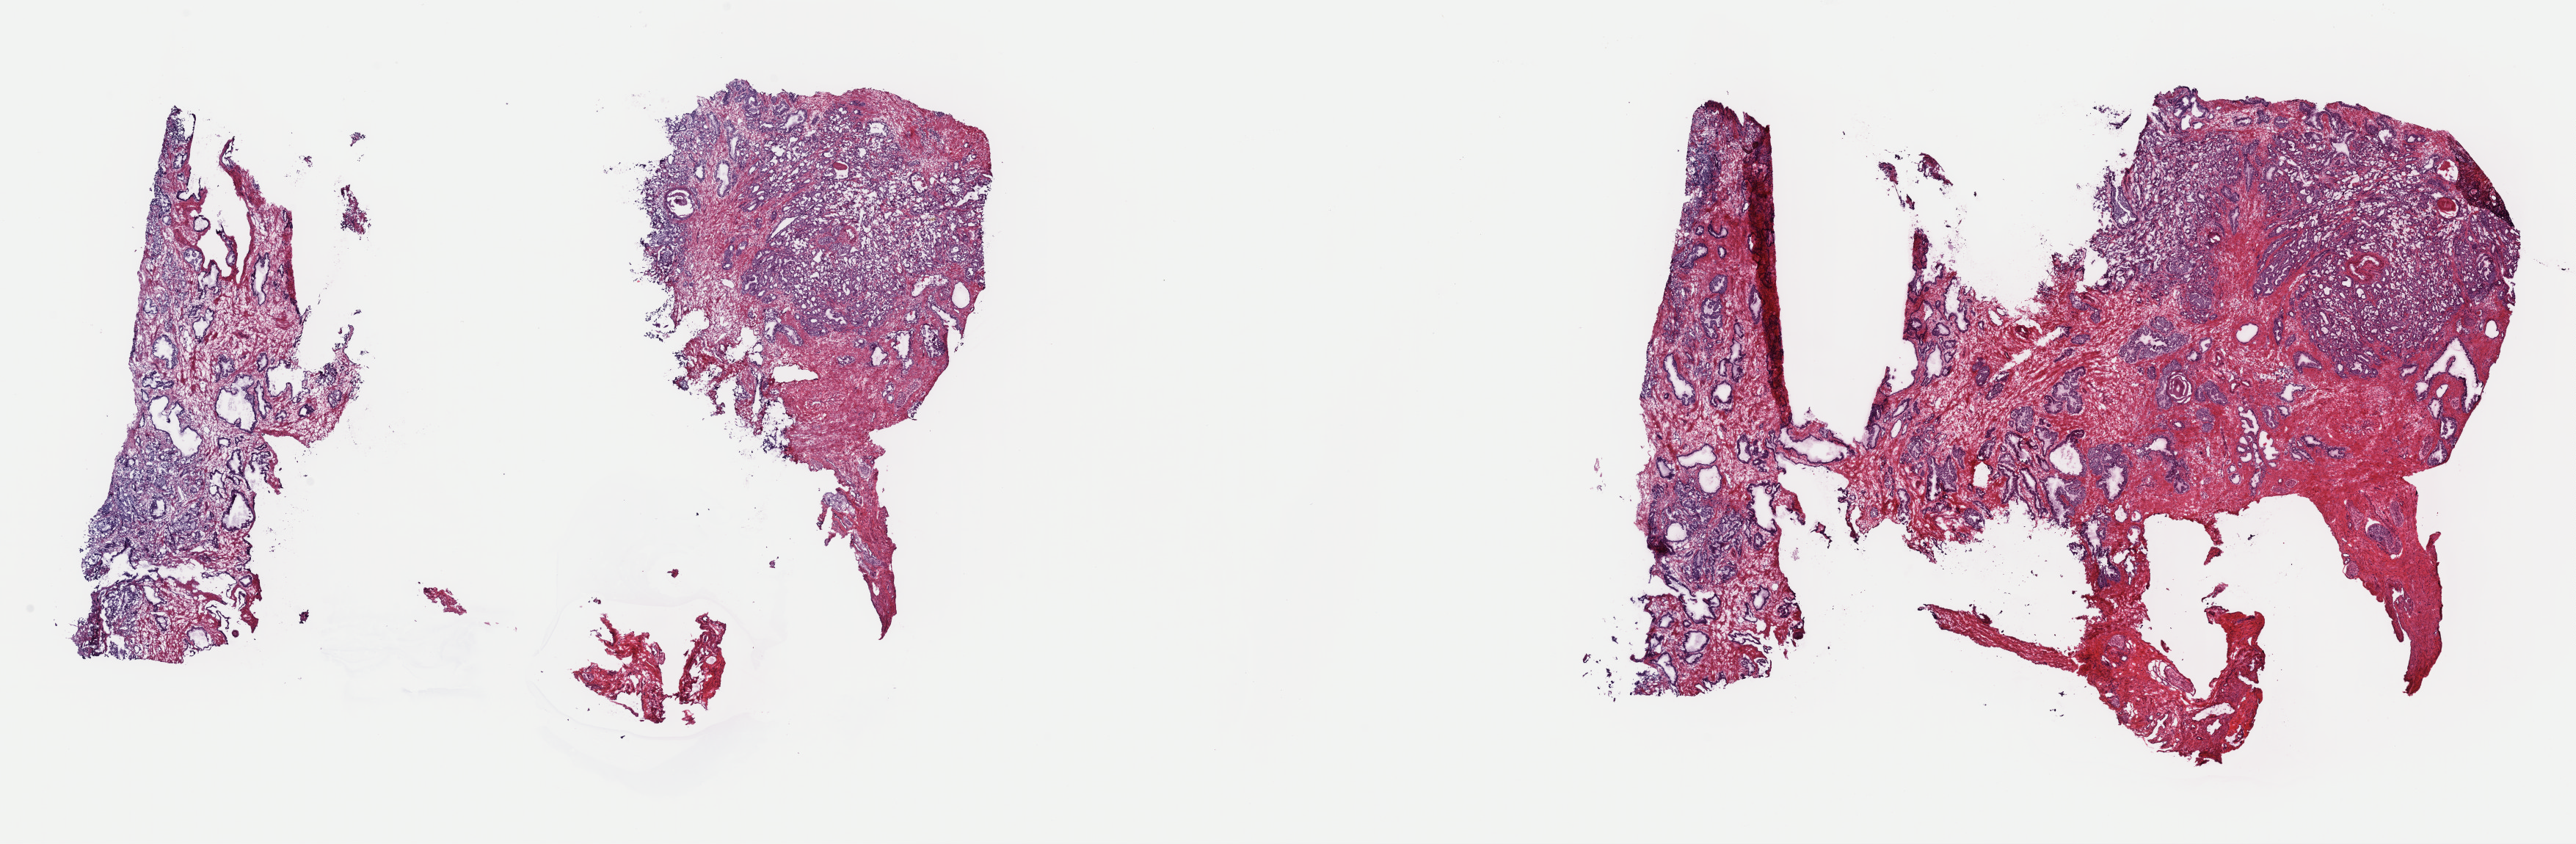
Digitized H&E tissue section (whole slide) — whole scanned area (about 27.7 x 9.1 mm) shown as a low-resolution overview. Frozen section from the top of the tissue portion. Primary tumour sample from the prostate. Male patient; age at initial diagnosis 70 years. Pathologist review of this section (percent, as recorded): tumour cells 60%, tumour nuclei 80%.
Pathologic diagnosis: Adenocarcinoma, NOS (prostate gland).